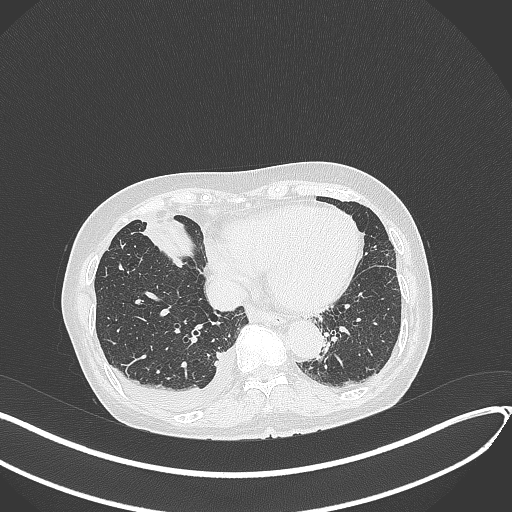
Chest CT, one axial slice; slice 113 of 418 in the series (ordered by position); lung window (W 1500 / L -600 HU); 1 mm slice thickness; 512 × 512 image matrix, field of view 400 × 400 mm. Female patient, age 75 years. Case-level facts recorded for this patient, not image findings: clinical TNM (as recorded): T2a N3 M0.
Outlined on this slice (bounding box drawn by a radiologist):
- lung tumour (recorded histology: adenocarcinoma): bounding box <142,214,202,260> (left, top, right, bottom; pixels)